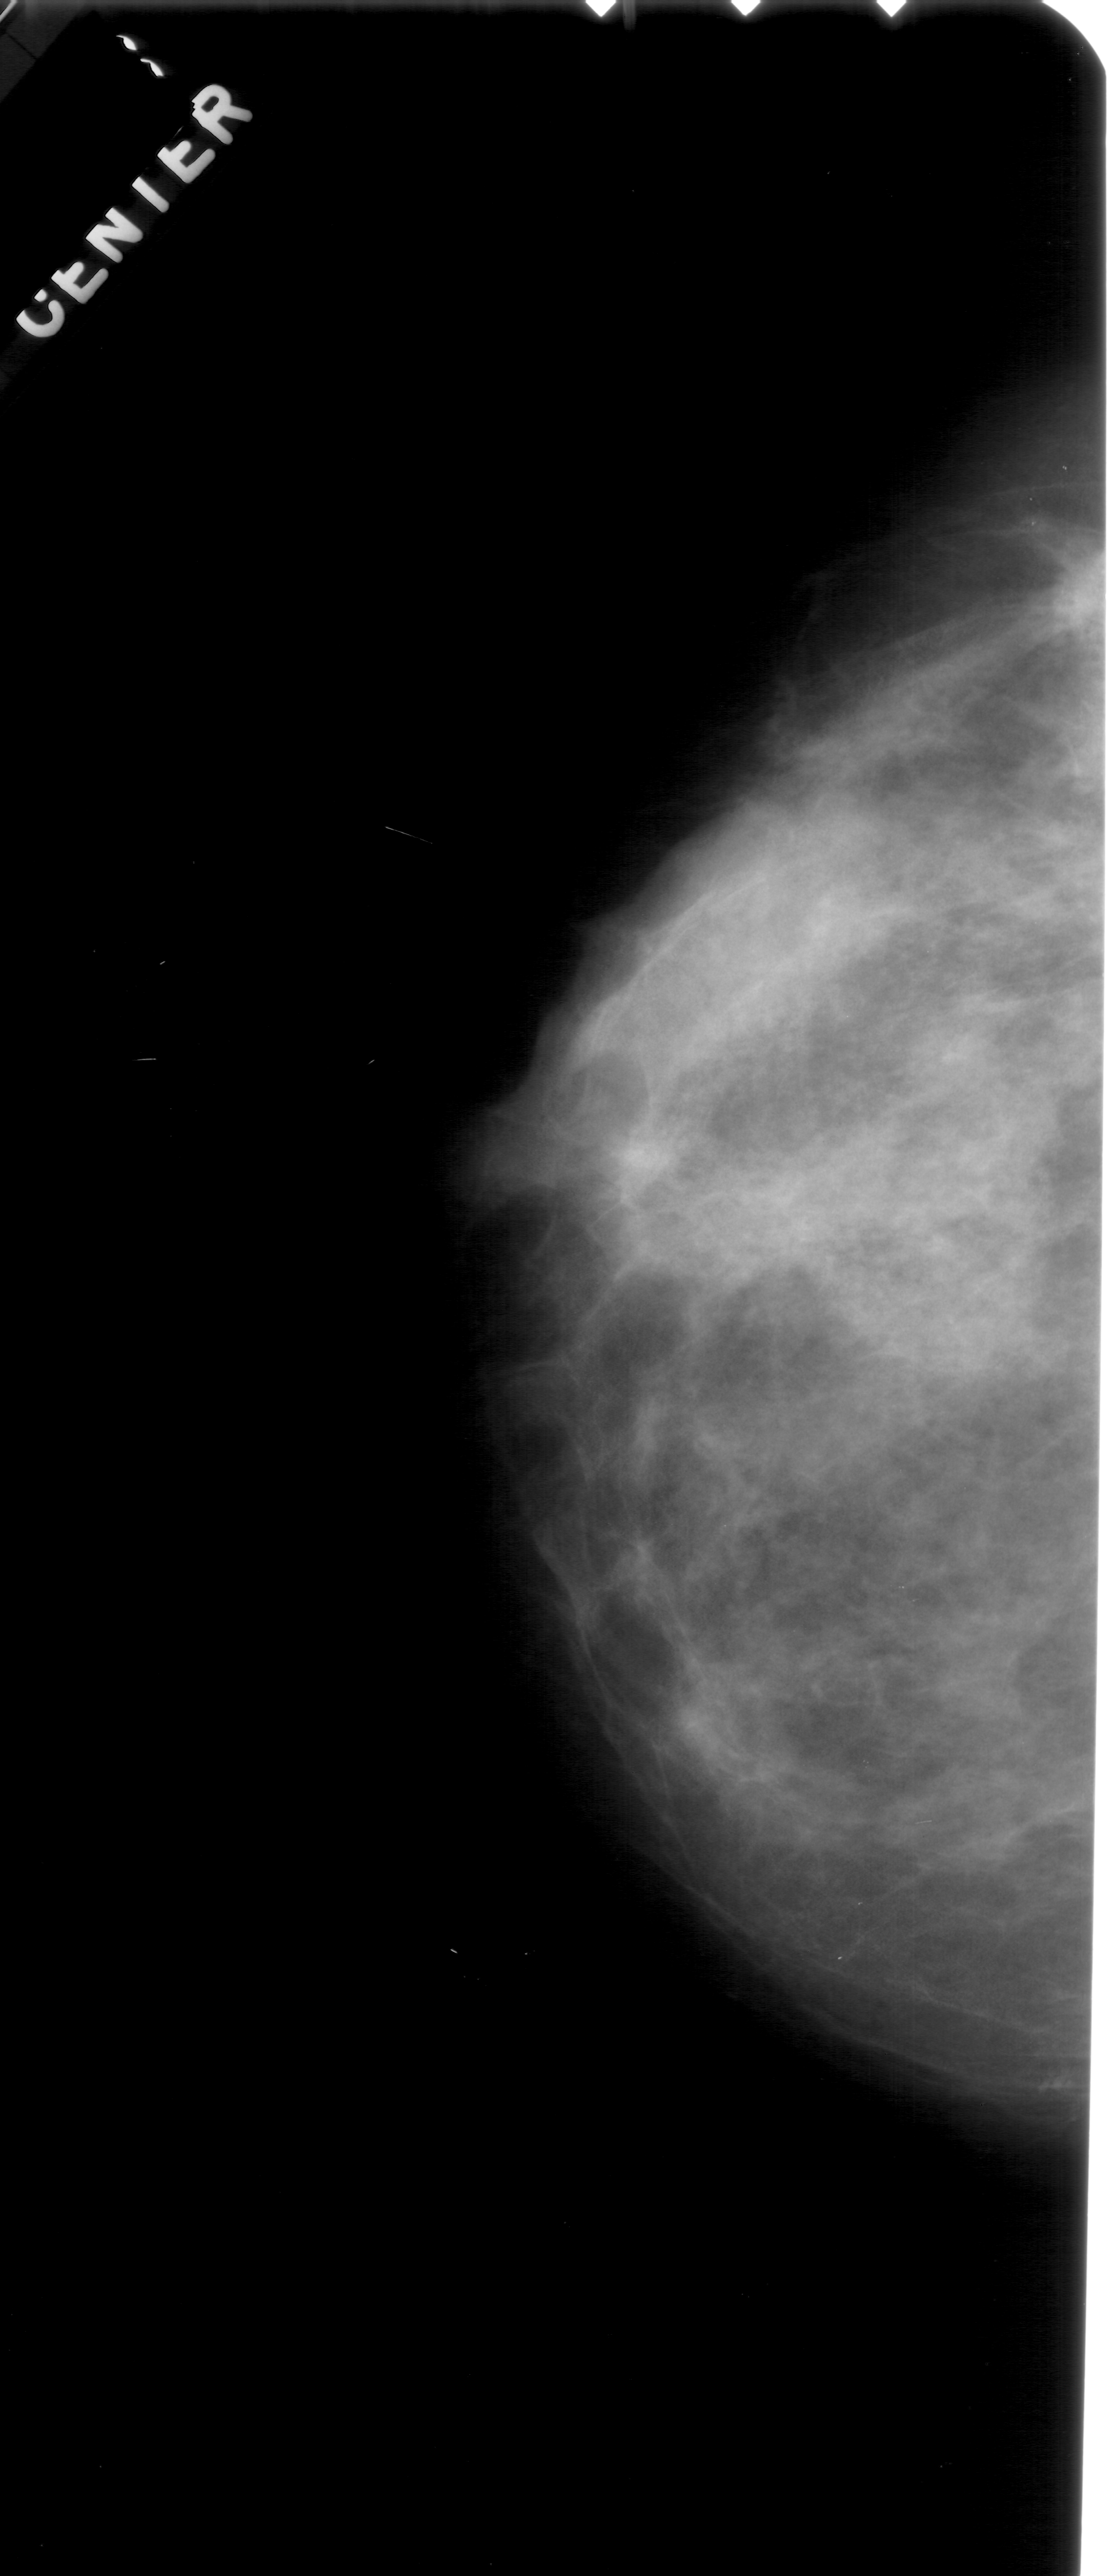
Scanned film-screen mammogram. Left breast. Craniocaudal (CC) view. Breast composition: extremely dense (BI-RADS density category 4 of 4). 1113 × 2576 image matrix.
Expert-marked regions of interest on this film, with their recorded descriptors:
- mass, shape irregular, margins spiculated; BI-RADS assessment category 4; pathology result (as recorded, not read from the image): malignant: bounding box (x1, y1, x2, y2) in pixels: (998, 548, 1105, 679)